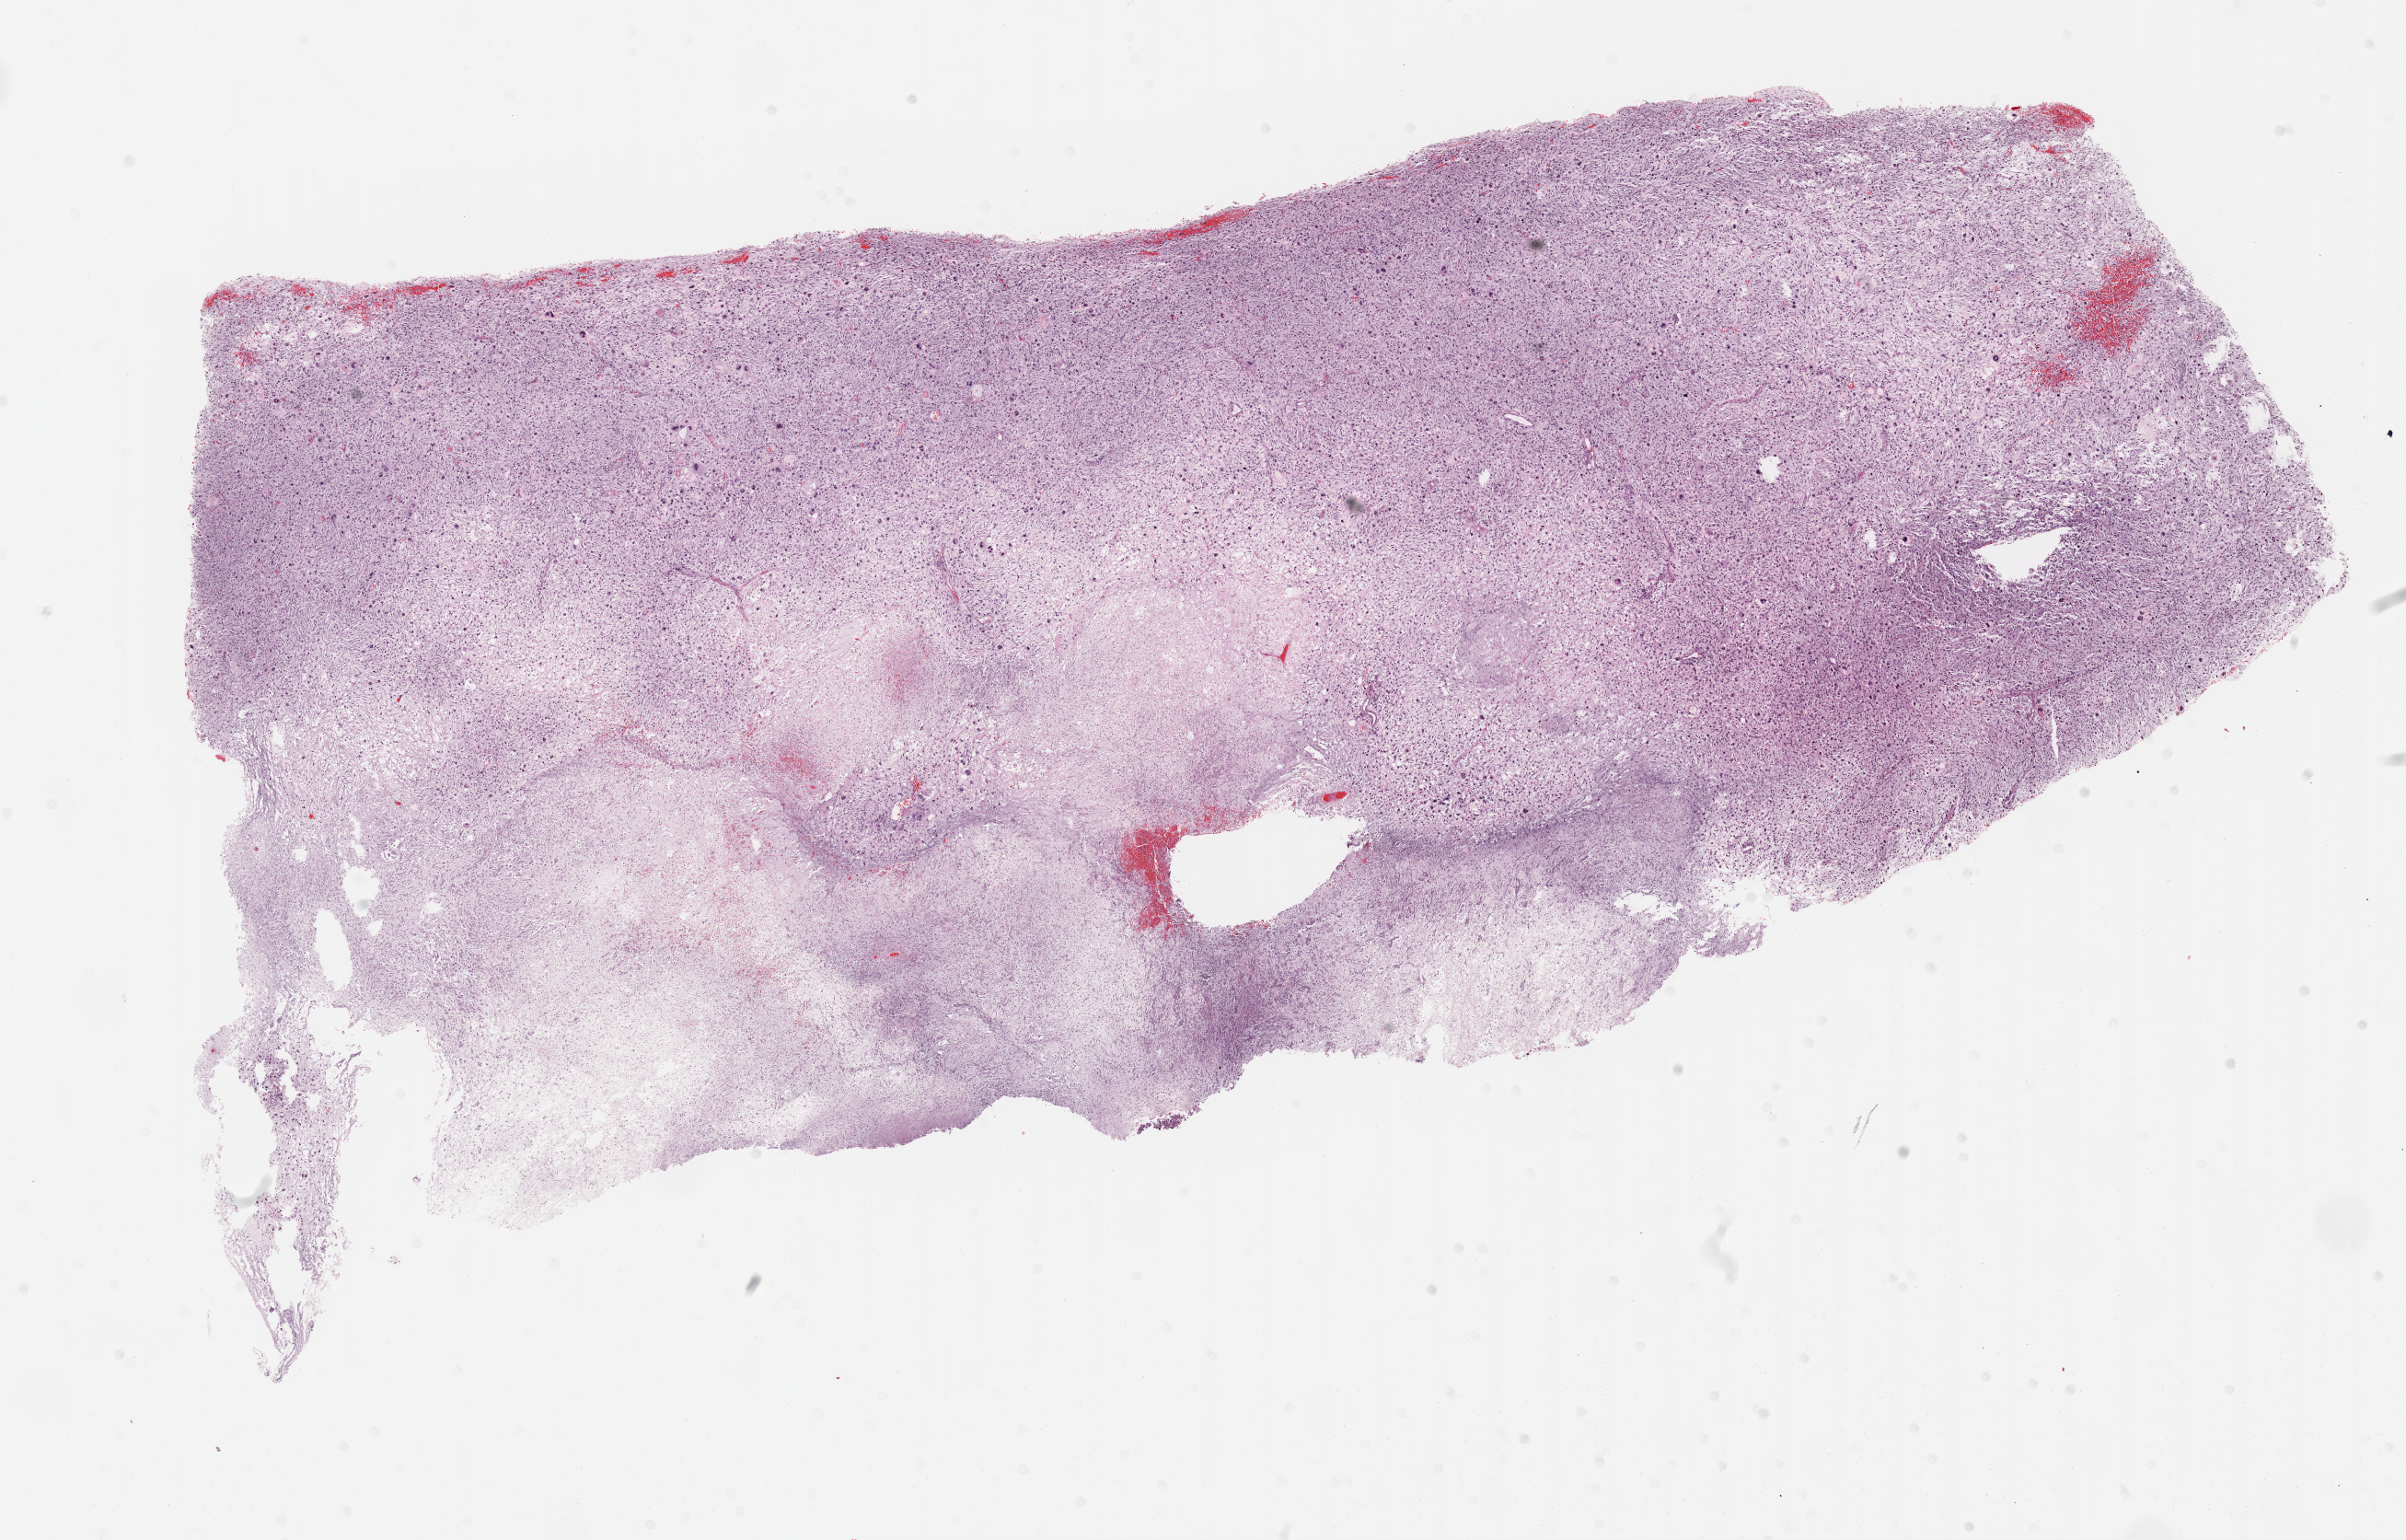
H&E whole-slide image, a low-resolution overview of the entire scanned area, about 21.1 x 13.5 mm; FFPE section; connective, subcutaneous and other soft tissues, primary tumour sample. Patient: male, age at initial diagnosis 74 years.
Histologic diagnosis: Fibromyxosarcoma (connective, subcutaneous and other soft tissues of lower limb and hip).